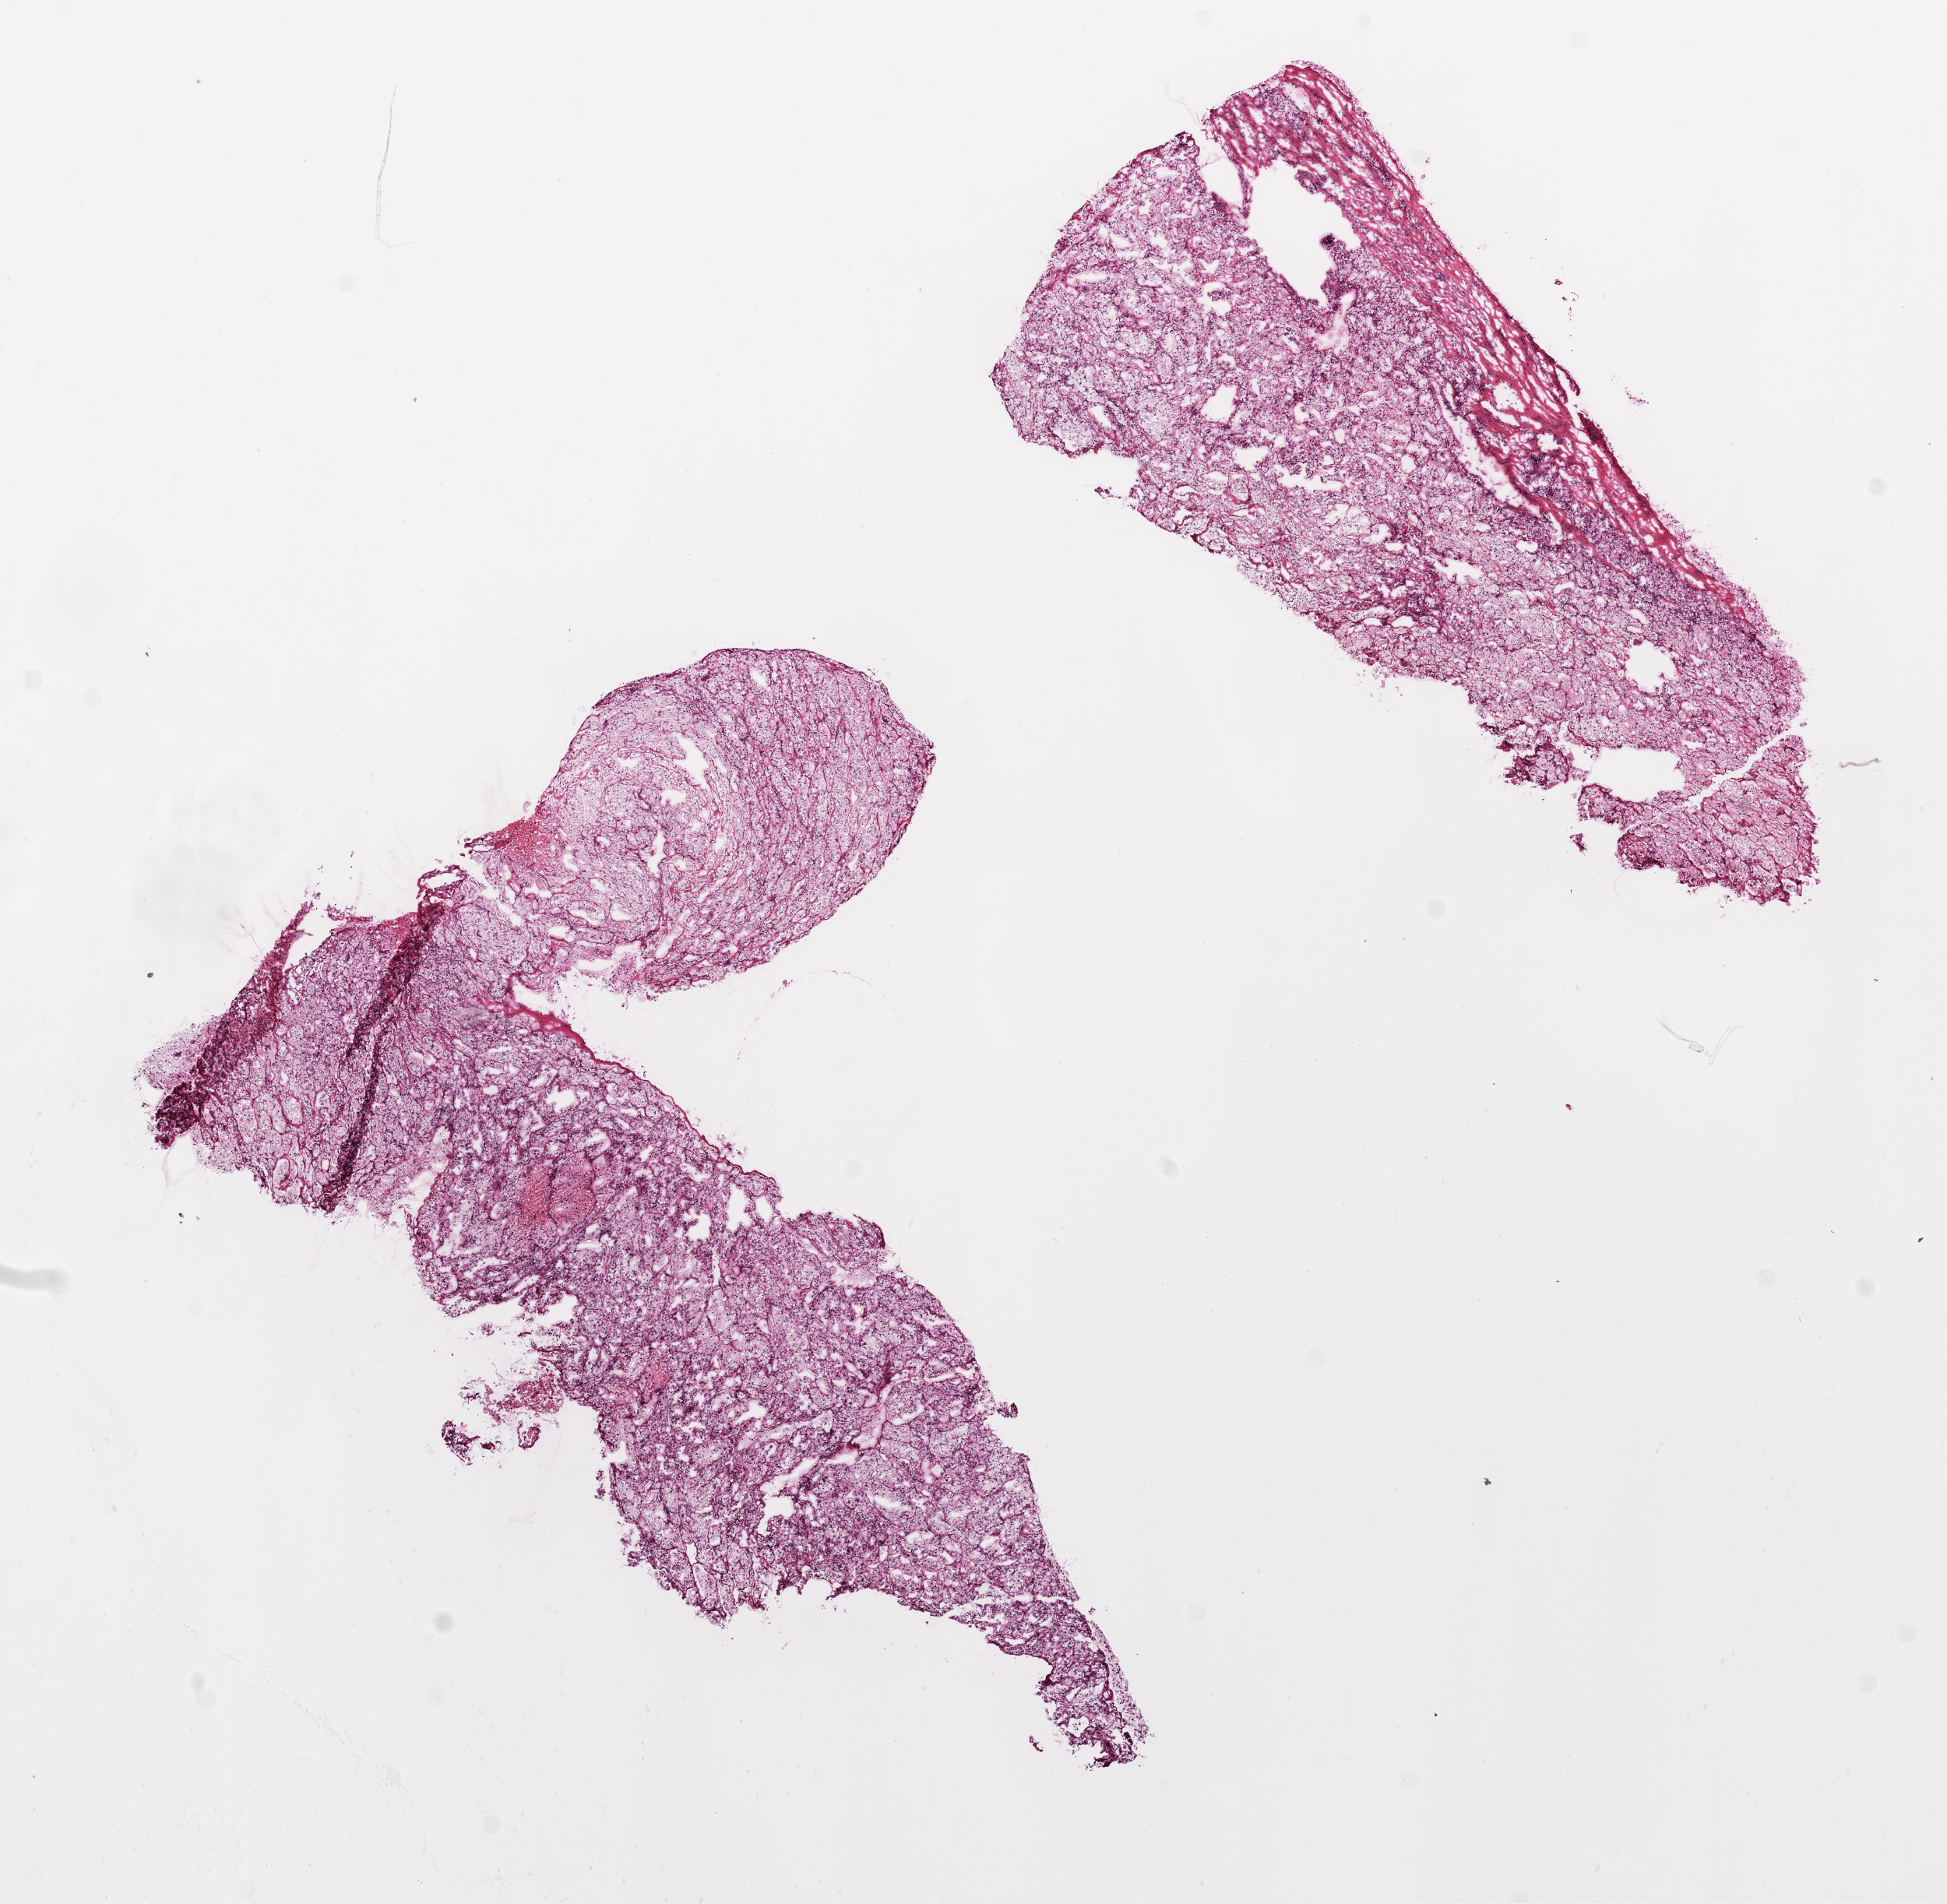
Whole-slide histology image, Hematoxylin and eosin (H&E) stained — shown as a low-resolution overview of the whole scanned area (about 10.0 x 9.8 mm). Frozen section from the top of the tissue portion. Kidney, primary tumour sample. Female patient; age at initial diagnosis 71 years. Histologic grade: G3 (poorly differentiated). Composition of this section per pathologist review: tumour cells 85%, tumour nuclei 80%, normal cells 0%, stromal cells 10%, necrosis 5%.
Diagnosis: Clear cell adenocarcinoma, NOS. AJCC pathologic stage: III.